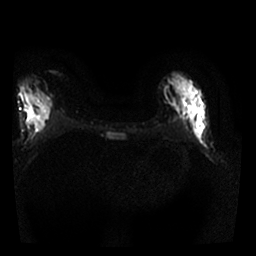
Breast MRI, one axial slice. Slice 11 of 25 in the series (ordered by position). Diffusion-weighted series; image 2 of 4 stored at this slice position (different b-values; order by instance number). 1.5 T. 4 mm slice thickness. 256 × 256 image matrix. Female patient.
Structures marked on this image (manually delineated by an expert):
- tumour on diffusion-weighted imaging: box from (x=186, y=94) to (x=205, y=144) px